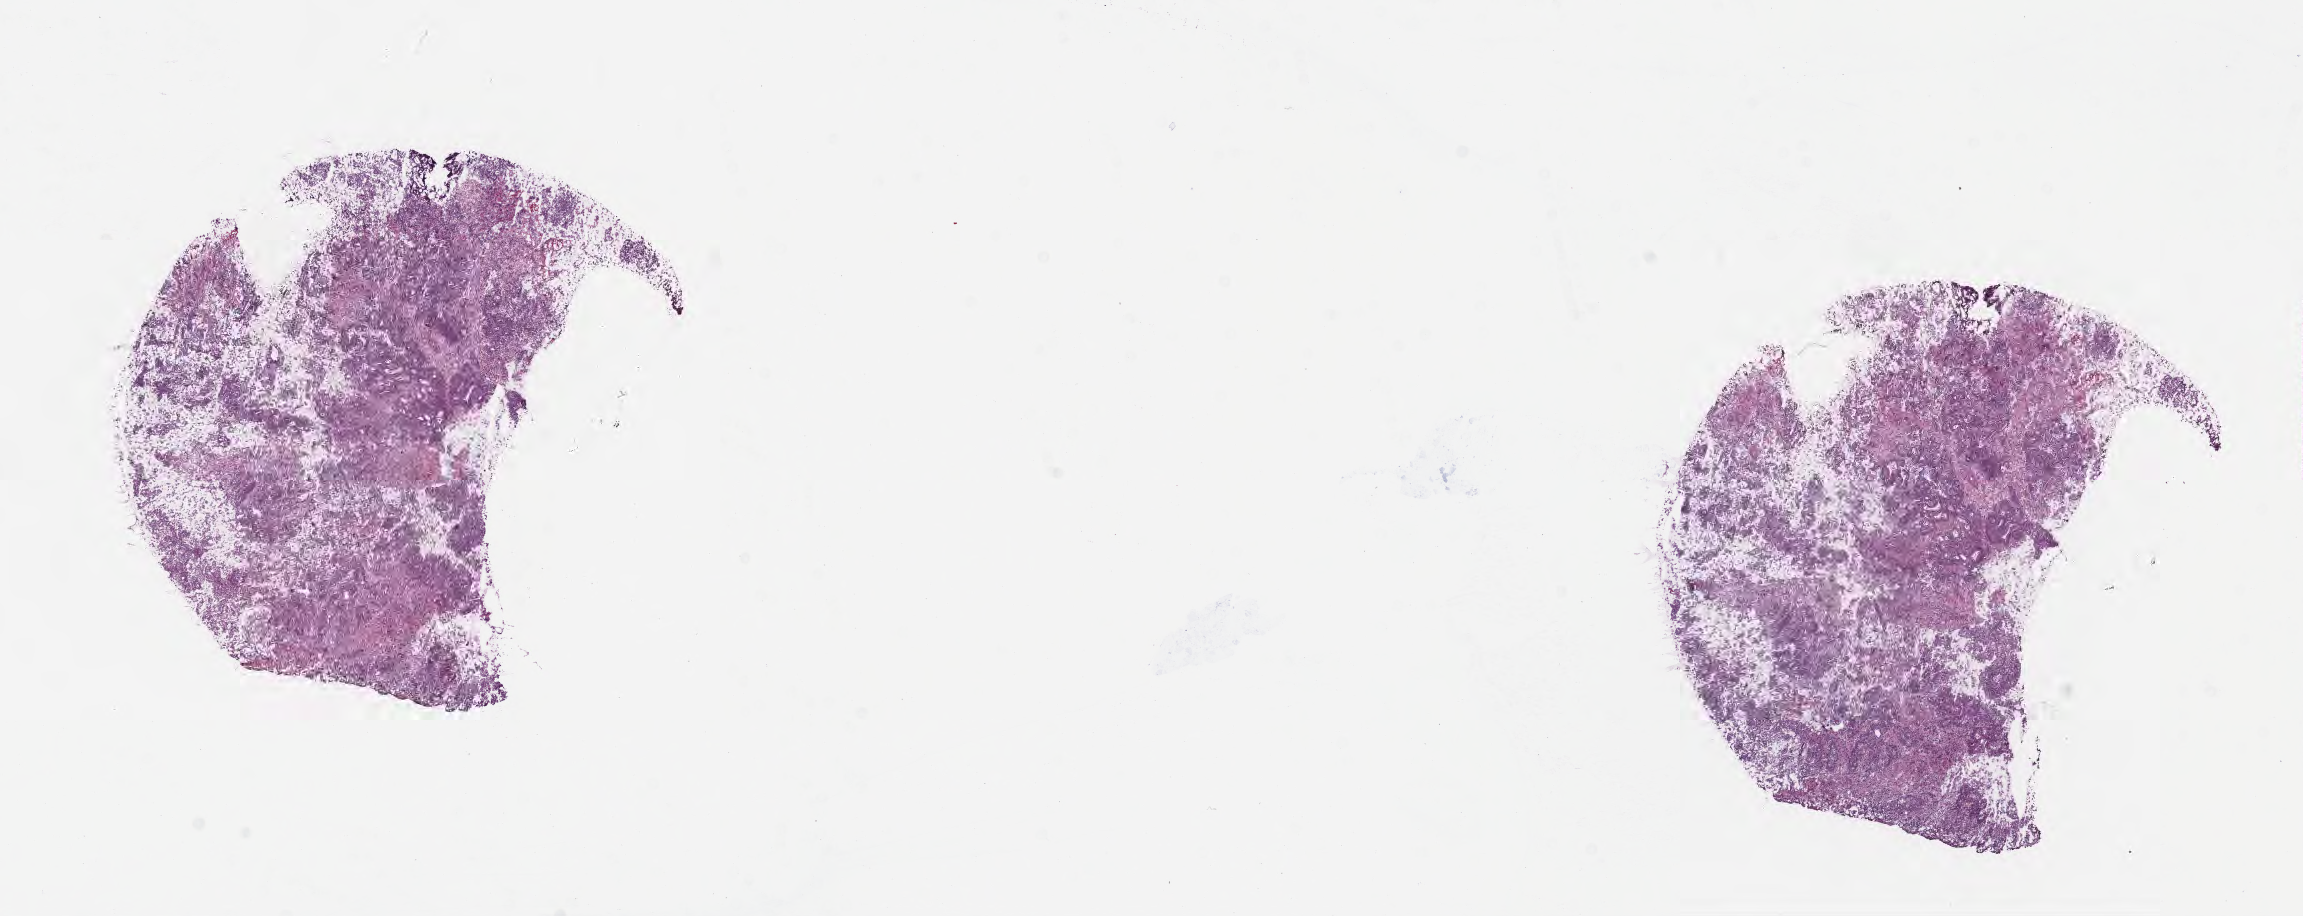
Haematoxylin and eosin whole-slide image, low-resolution overview of the scanned area, about 18.6 x 7.4 mm, frozen section, primary tumor, anatomic site: cecum. Male patient; age at initial diagnosis 74 years. Tumor grade: GB (borderline). Slide review estimates, as recorded: tumor cells 85%, tumor nuclei 85%, stromal cells 15%, necrosis 0%, normal cells 0%. Inflammatory infiltration, as recorded: lymphocyte infiltration 3%, monocyte infiltration 2%, neutrophil infiltration 6%.
- diagnosis: Adenocarcinoma, NOS
- AJCC pathologic stage: Stage IIIB
- section: bottom of the tissue portion